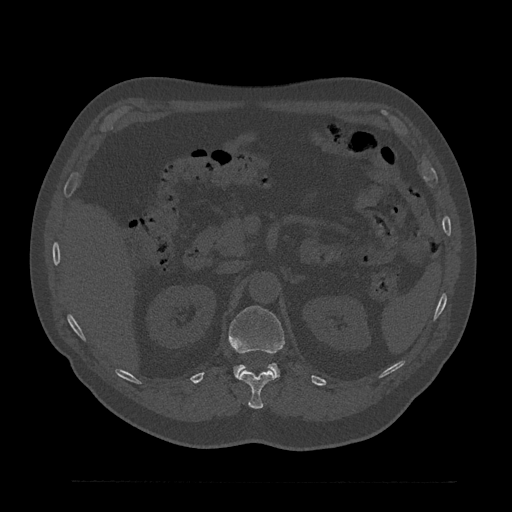
CT including the spine, one axial slice; position 197 of 797 along the scan axis; reconstruction kernel Br40s/3; 120 kVp; bone window (W 1800 / L 400 HU); 0.5 mm slice thickness; 512 × 512 image matrix. Male patient, age 61 years. Case-level facts recorded for this patient, not image findings: primary cancer: prostate.
Structures marked on this image (semi-automatically segmented with operator editing):
- L1 vertebra: bounding box <229,306,284,377> (left, top, right, bottom; pixels)
- T12 vertebra: <237,370,276,409>